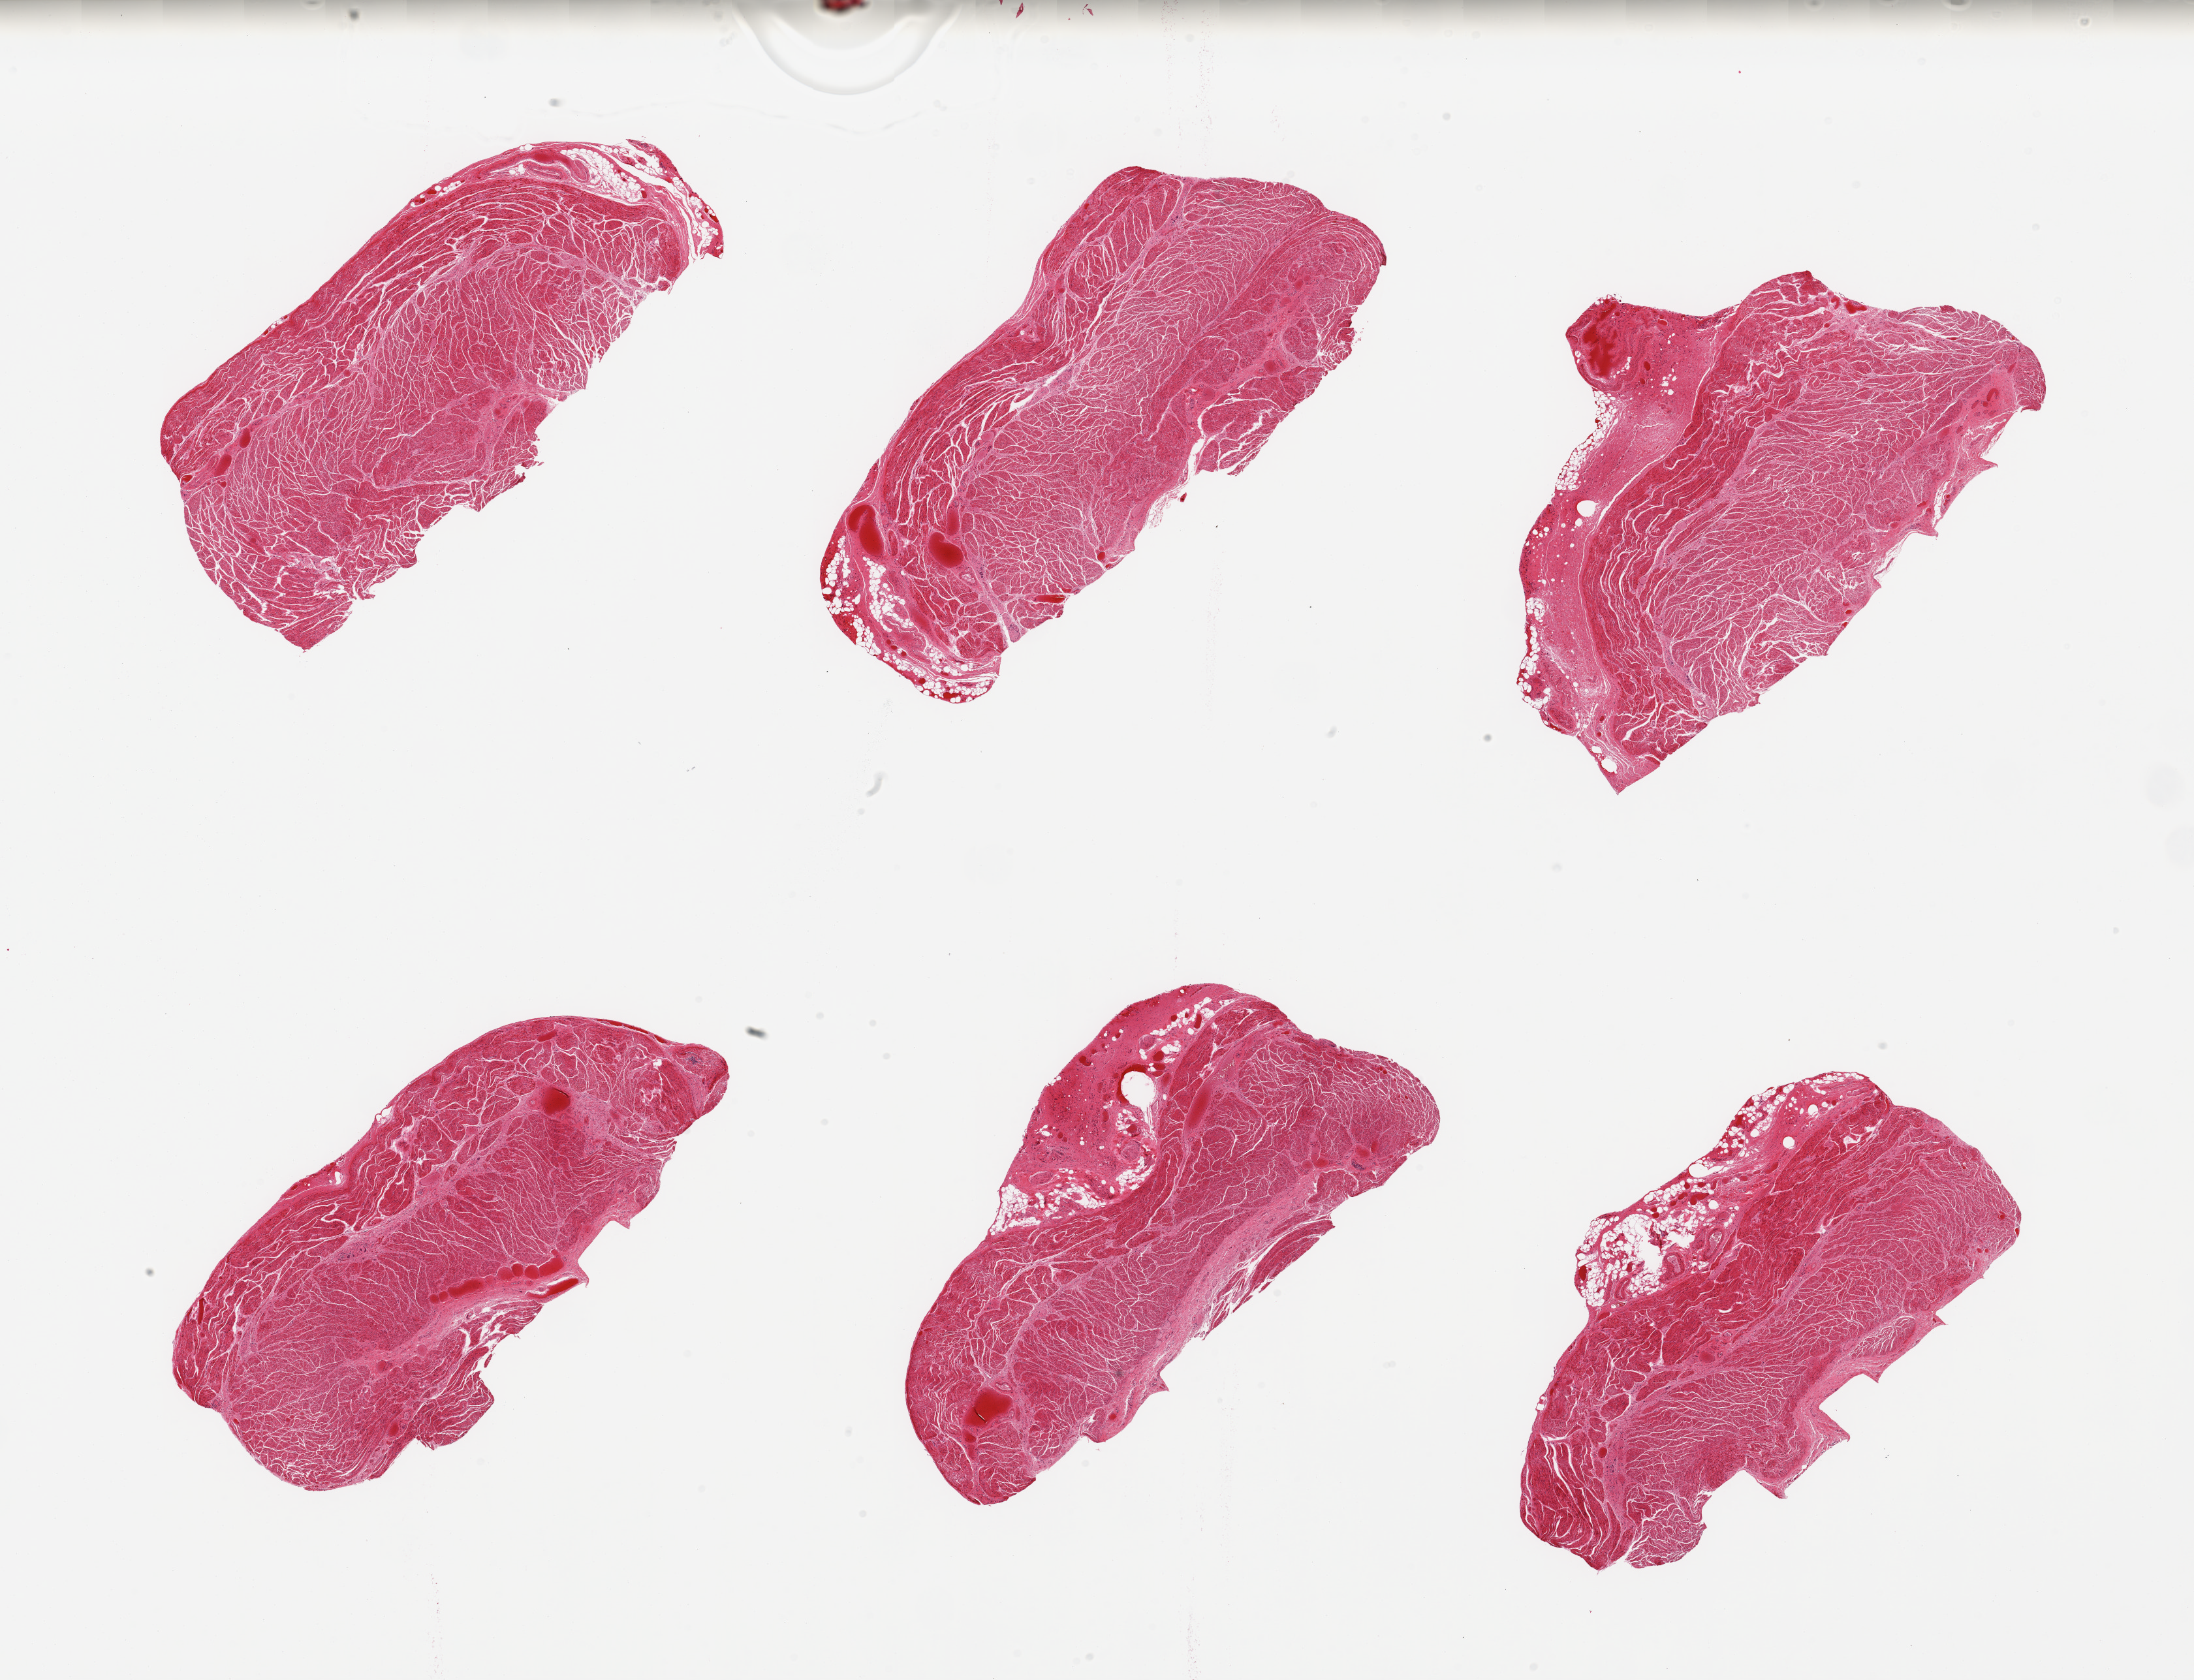
Hematoxylin and eosin (H&E) whole-slide image, brightfield — shown as a low-resolution overview of the whole scanned area (about 26.6 x 20.4 mm), PAXgene-fixed, paraffin-embedded tissue, target tissue: gastroesophageal junction, donor tissue sample. Donor: male.
Review note (as recorded): 6 pieces; focal fatty adventitia up to 1 mm.